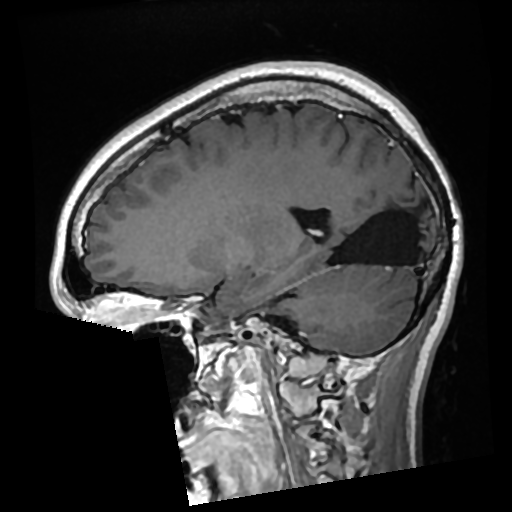
Brain MRI from a brain-tumour surgery series, one sagittal slice. T1-weighted post-contrast. 512 × 512 image matrix, field of view 250 × 250 mm. From the clinical record (not read from this slice): histopathology: Glioma with ependymal features; WHO grade: 2; tumour location: Left Parietal.
Structures marked on this image (outlined manually by an expert reader):
- previous resection cavity: box from (x=330, y=188) to (x=422, y=266) px